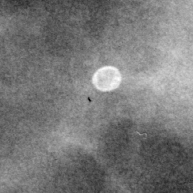
Crop from a digitized film mammogram around one marked abnormality, left breast, CC view, BI-RADS breast density category 3 (scale 1–4).
- Finding: calcifications, morphology lucent center; BI-RADS assessment category 2; benign; no additional work-up was recommended (benign without callback).